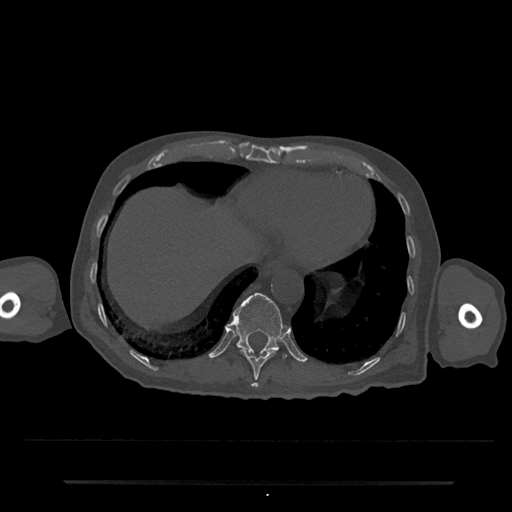
CT including the spine, one axial slice. Slice 283 of 797 in the series (ordered by position). Reconstruction kernel Br40s/3. Bone window (W 1800 / L 400 HU). 512 × 512 image matrix. Male patient, age 74 years. Case-level facts recorded for this patient, not image findings: primary cancer: prostate.
Outlined on this slice (semi-automatic segmentation, software-assisted and operator-edited):
- T10 vertebra: box from (x=239, y=349) to (x=277, y=388) px
- T11 vertebra: (x=228, y=292)–(x=286, y=358)